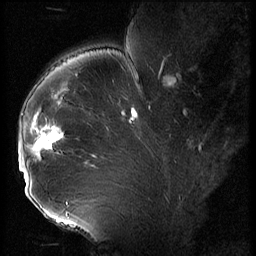
Breast MRI (dynamic contrast-enhanced), one sagittal slice; position 39 of 56 along the scan axis; 3 images stored at this slice position (order not interpretable as contrast timing); 1.5 T; TE 4.2 ms, TR 9 ms; 256 × 256 image matrix, field of view 180 × 180 mm. Female patient, age 43 years. Case-level facts recorded for this patient, not image findings: setting: breast cancer imaged before/during neoadjuvant chemotherapy; receptor status: HER2-positive.
Structures marked on this image (semi-automatically segmented with operator editing):
- analysis volume of interest (the breast-tissue region the enhancement analysis was run in; not a lesion): box from (x=19, y=92) to (x=74, y=211) px
- tumour enhancement mask (voxels above the 140 % enhancement threshold inside the analysis volume of interest): (x=20, y=128)–(x=64, y=184)